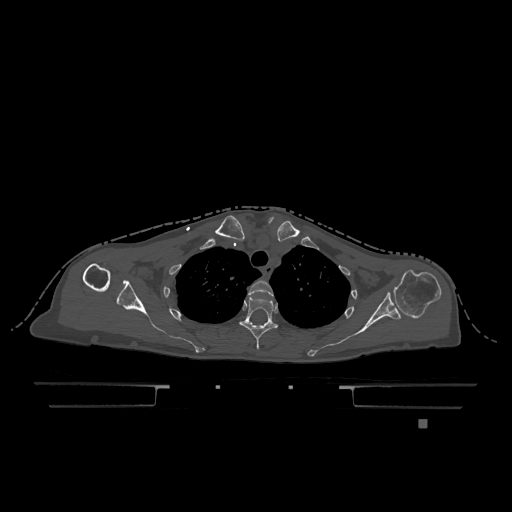
CT including the spine, one axial slice. Slice 927 of 1317 in the series (ordered by position). Bone window (W 1800 / L 400 HU). 0.5 mm slice thickness. 512 × 512 image matrix, field of view 500 × 500 mm. Female patient, age 74 years. Case-level facts recorded for this patient, not image findings: primary cancer: lung.
Outlined on this slice (semi-automatic segmentation, software-assisted and operator-edited):
- T2 vertebra: bounding box <248,281,274,297> (left, top, right, bottom; pixels)
- T3 vertebra: <238,297,278,349>